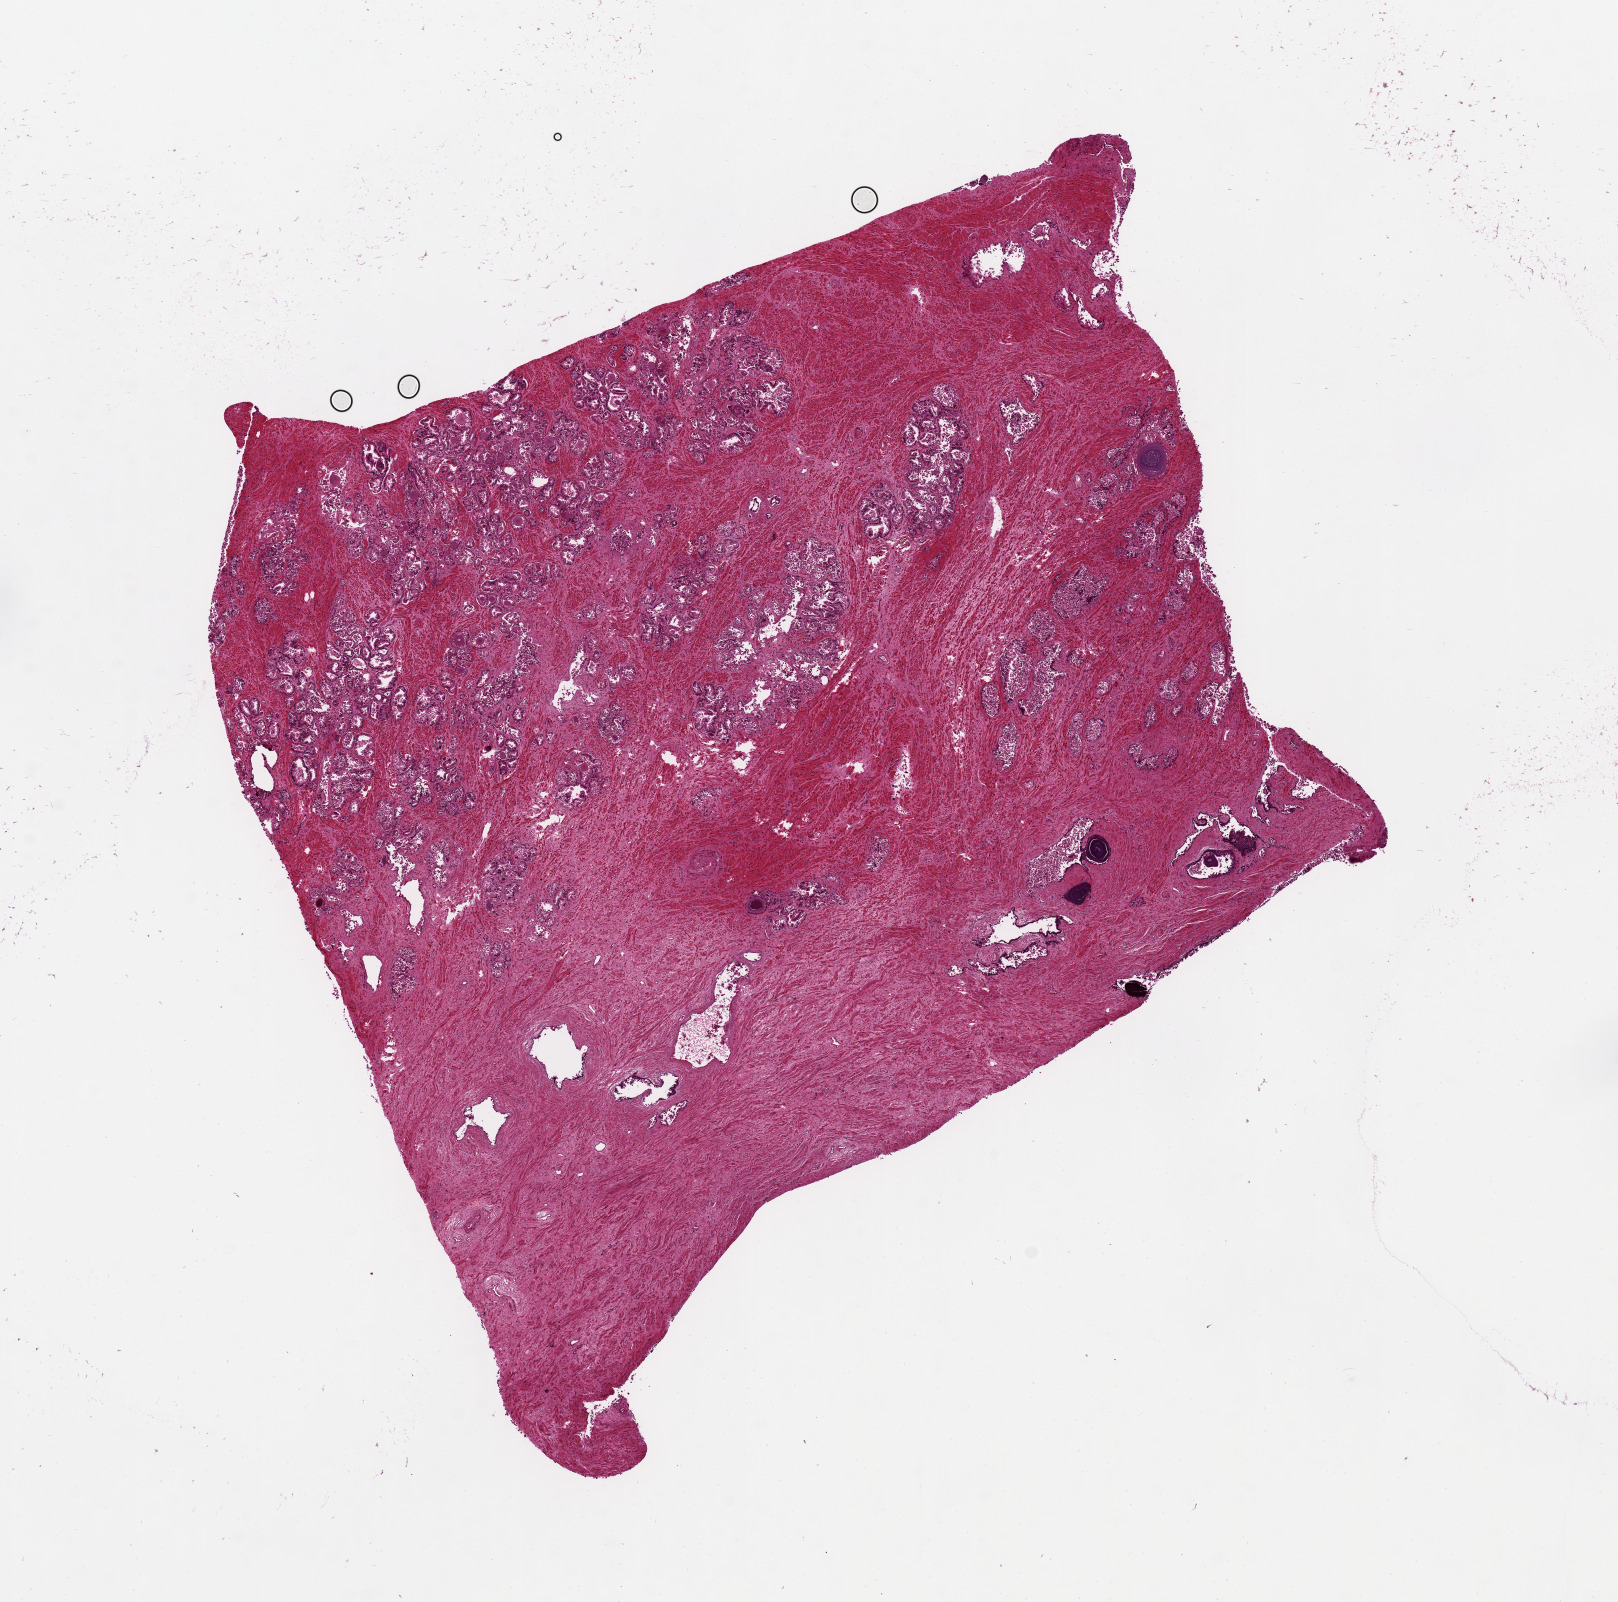
Hematoxylin and eosin (H&E) whole-slide image, brightfield, whole scanned area (about 12.8 x 12.7 mm, from a 20x scan) shown as a low-resolution overview, PAXgene-fixed, paraffin-embedded tissue, target tissue: prostate, tissue donor sample. Male donor.
Reviewer comment on this tissue sample: 8x7 mm. Hyperplasia. Stroma 50%.